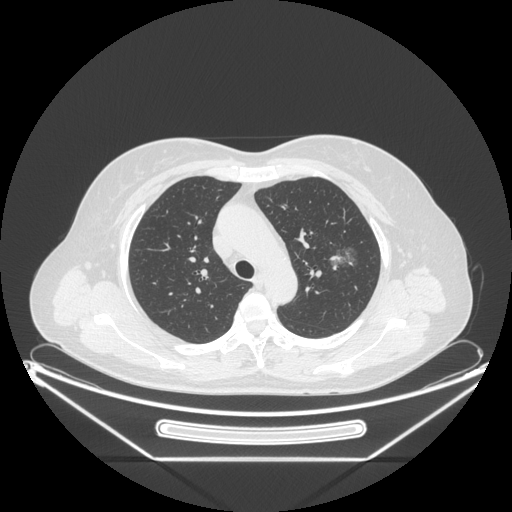
Chest CT, one axial slice; position 155 of 226 along the scan axis; 120 kVp; lung window (W 1500 / L -600 HU); 512 × 512 image matrix, field of view 447 × 447 mm. Female patient, age 54 years. From the clinical record (not read from this slice): clinical TNM (as recorded): T1c N0 M0; histopathological grade: G1.
Annotated regions visible in this slice (bounding box drawn by a radiologist):
- lung tumour (recorded histology: adenocarcinoma): box from (x=322, y=239) to (x=366, y=277) px